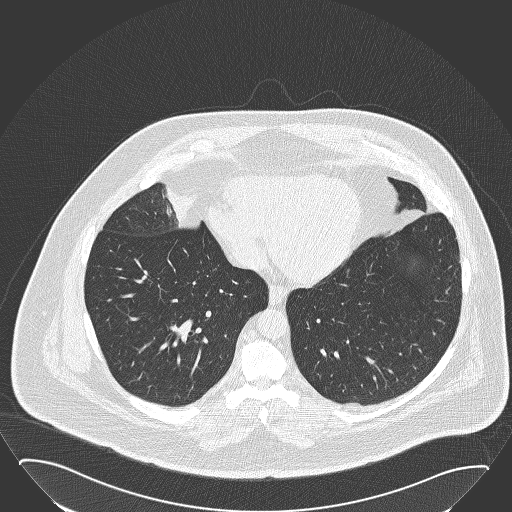
Low-dose screening chest CT, one axial slice; position 58 of 168 along the scan axis; reconstruction kernel B50f; 120 kVp; lung window (W 1500 / L -600 HU); 512 × 512 image matrix, field of view 432 × 432 mm.
Annotated regions visible in this slice (outlined manually by an expert reader):
- lesion 1 (tumor, hilum of right lung): bounding box (x1, y1, x2, y2) in pixels: (163, 187, 197, 229)